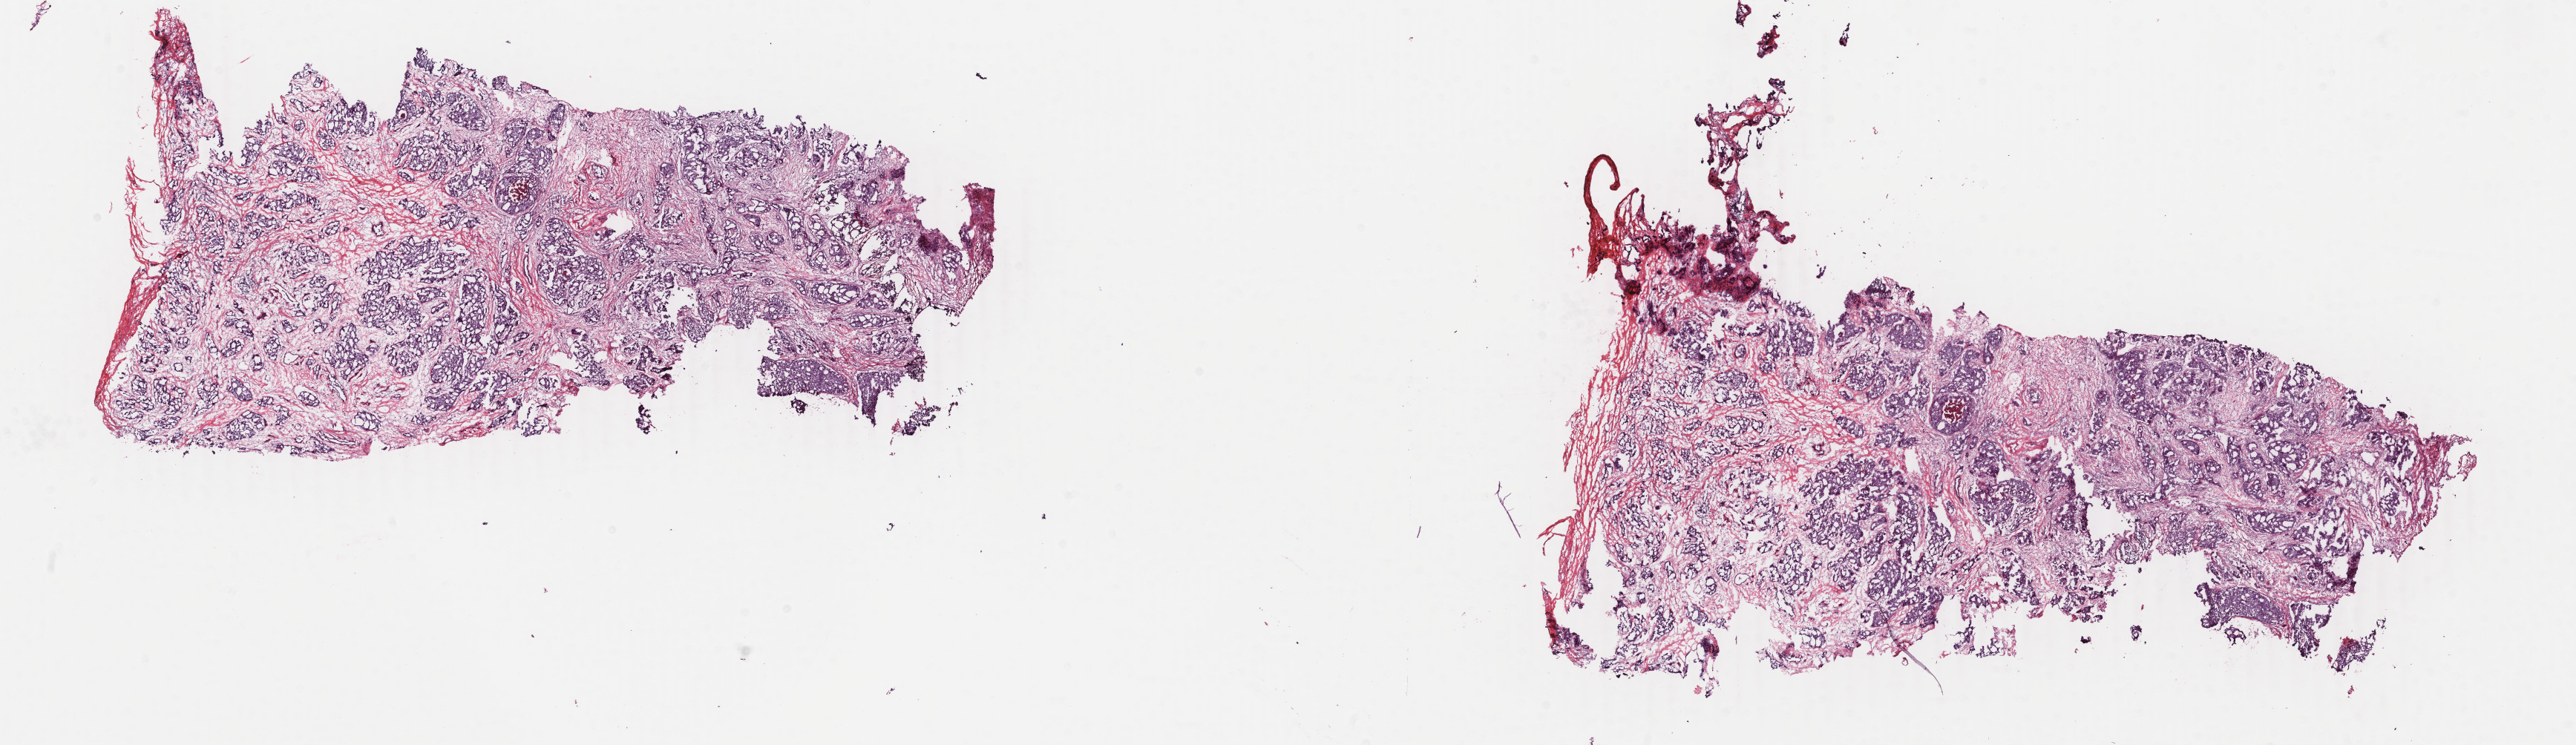
Whole-slide histology image, Hematoxylin and eosin (H&E) stained, a low-resolution overview of the entire scanned area, about 27.6 x 8.0 mm. Frozen section. Sample: primary tumour, breast. Female patient; age at initial diagnosis 54 years. Composition of this section per pathologist review: tumour cells 60%, tumour nuclei 60%, normal cells 0%, stromal cells 40%, necrosis 0%. Infiltration values recorded for this section: lymphocyte infiltration 60%, monocyte infiltration 30%, neutrophil infiltration 0%.
AJCC pathologic stage: I (4th edition). Diagnosis: Cribriform carcinoma, NOS.